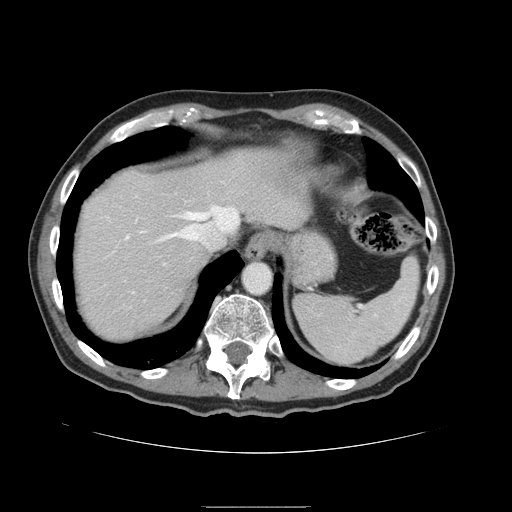
Contrast-enhanced abdominal CT, one axial slice; slice 126 of 168 in the series (ordered by position); intravenous contrast given; soft-tissue window (W 400 / L 40 HU); 2.5 mm slice thickness; 512 × 512 image matrix, field of view 386 × 386 mm. Male patient, age 74 years. From the clinical record (not read from this slice): diagnosis: colorectal cancer liver metastases, imaged before liver resection; multiple liver metastases: no; largest metastasis: 14.5 cm; chemotherapy before resection: no.
Annotated regions visible in this slice (manually delineated by an expert):
- hepatic veins: bounding box [x1, y1, x2, y2] px = [158, 206, 238, 246]
- liver: [73, 148, 311, 343]
- planned liver remnant (the part of the liver to remain after resection): [73, 147, 309, 343]